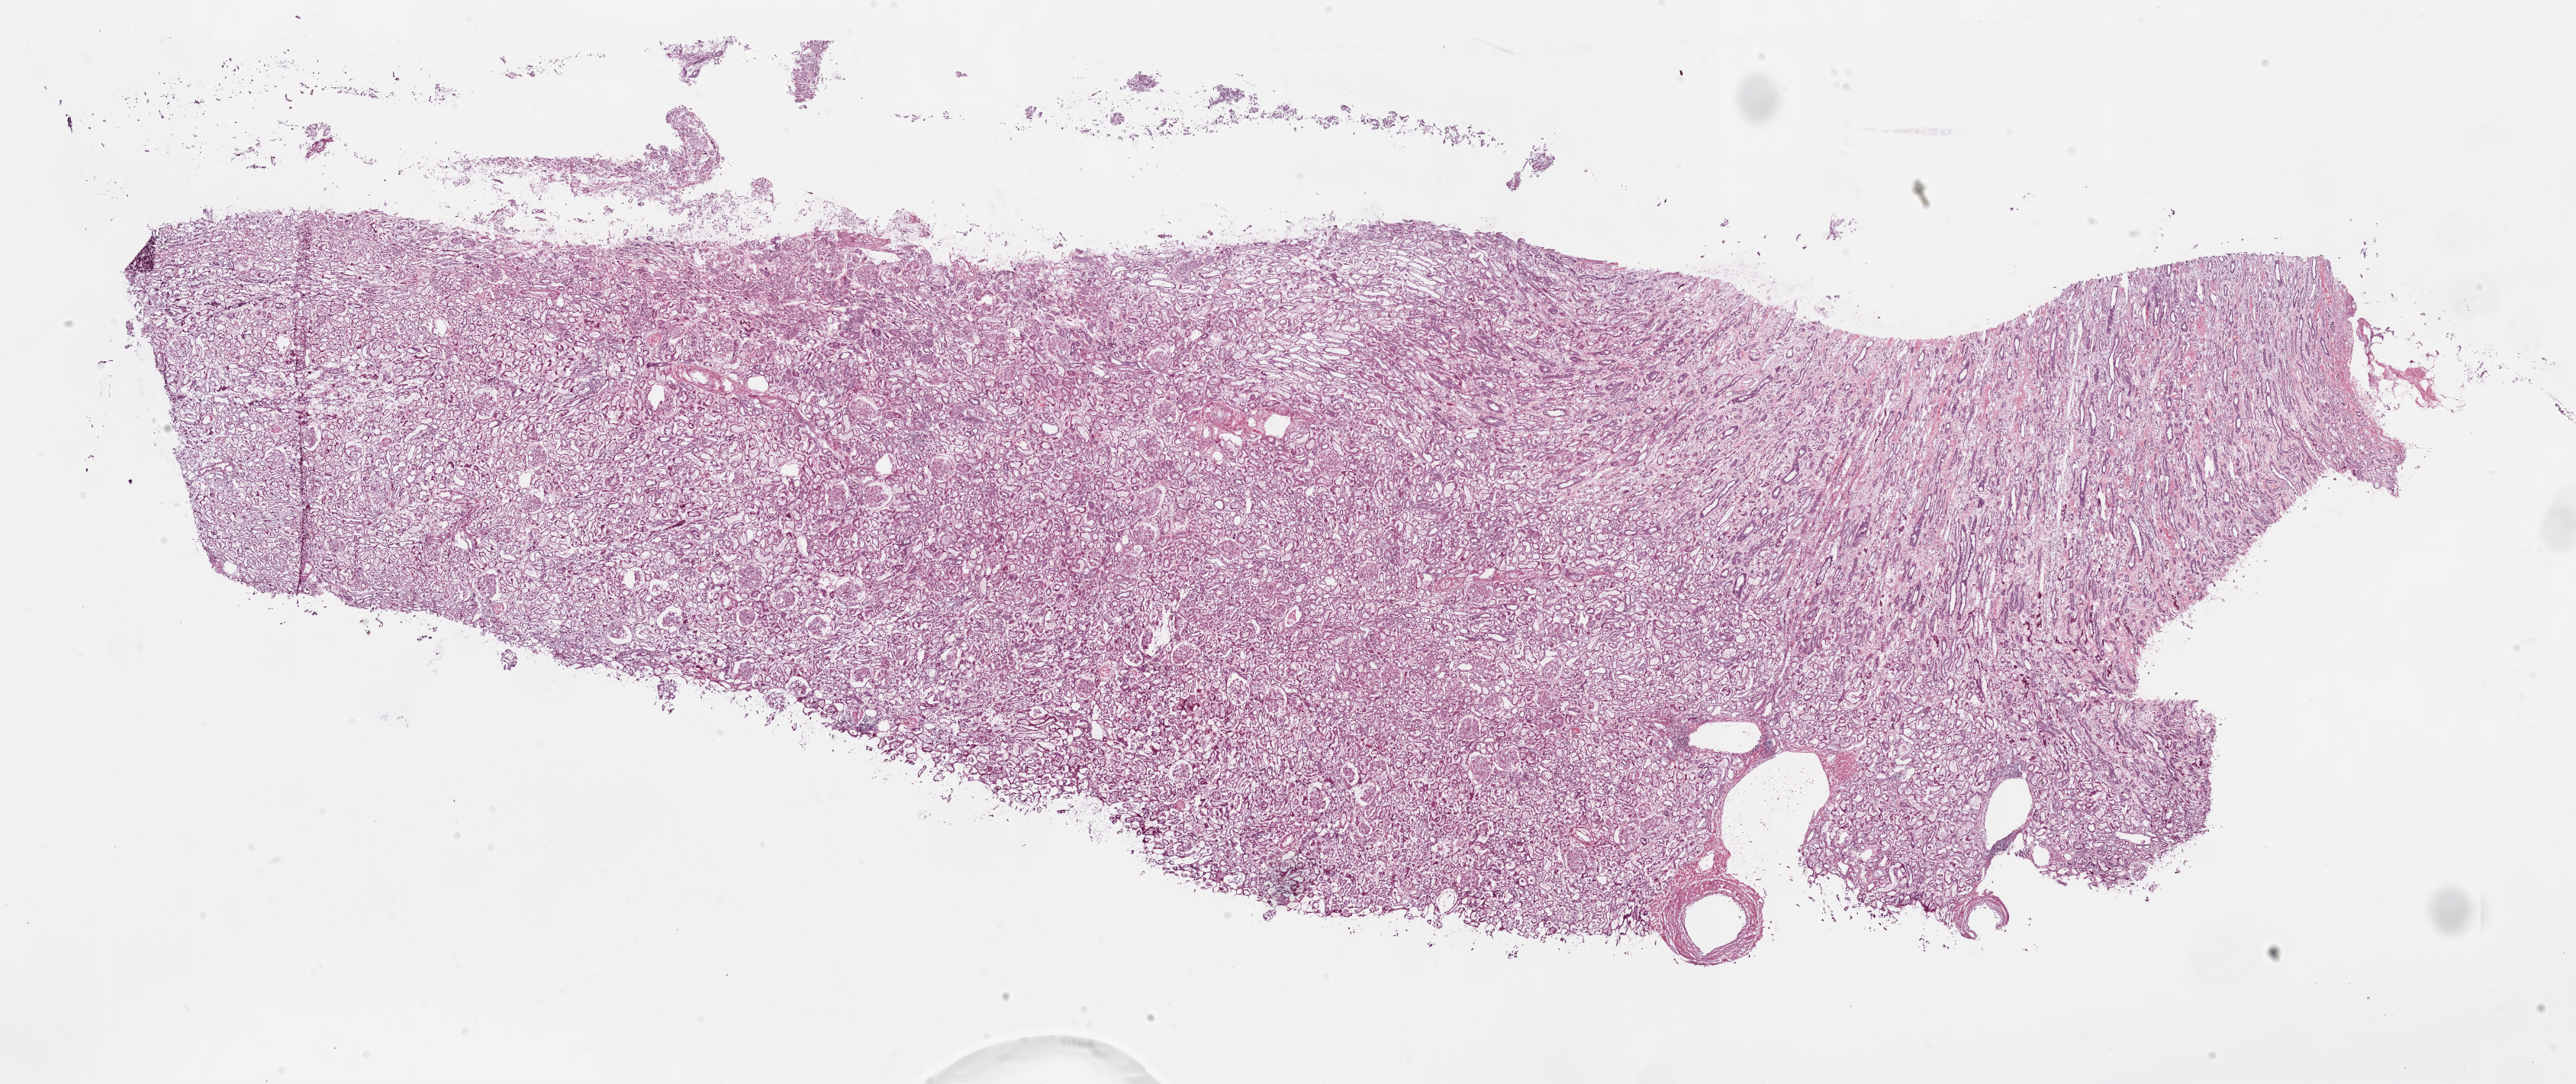
Whole-slide histology image, H&E-stained, low-resolution overview of the scanned area, about 26.8 x 11.3 mm, frozen section from the bottom of the tissue portion, solid tissue normal (non-tumour tissue) sample from the kidney. Male patient; age at initial diagnosis 63 years.
This section: solid tissue normal sample (biorepository sample class). Patient diagnosis: Clear cell adenocarcinoma, NOS.